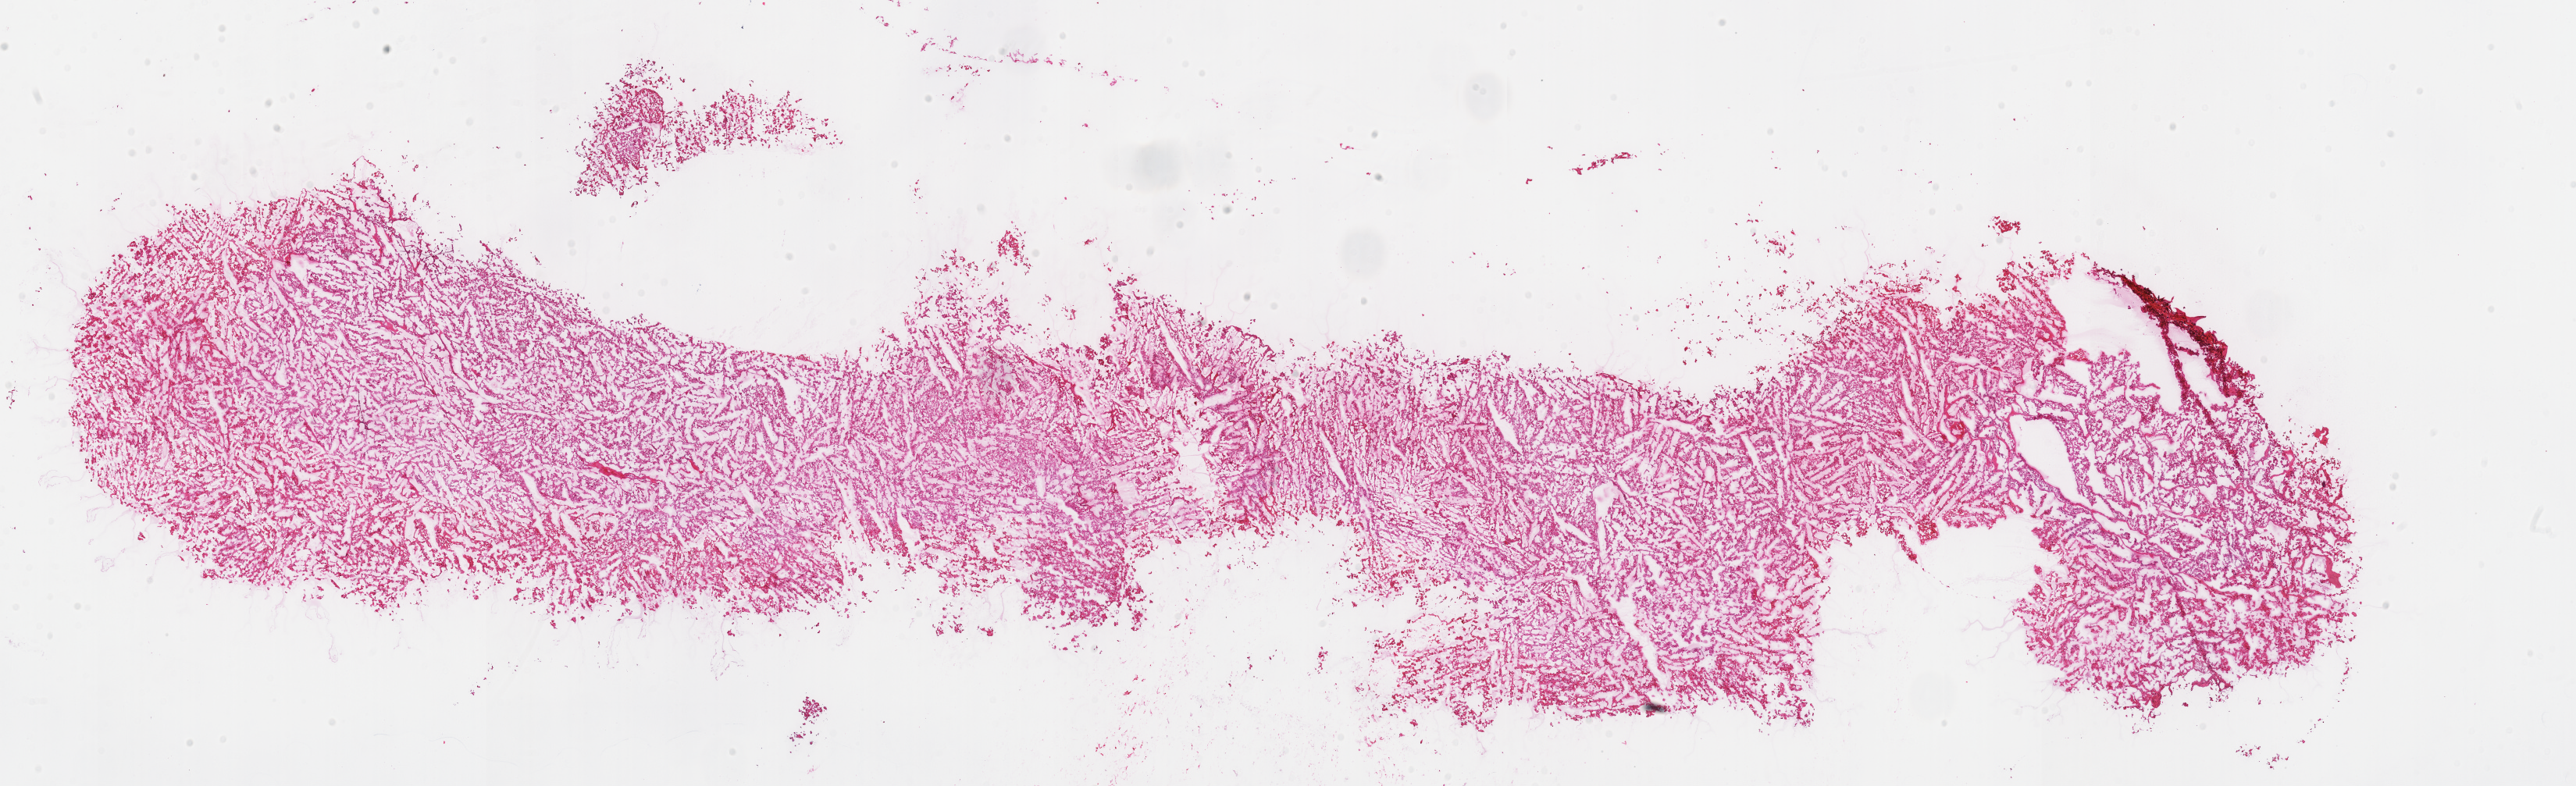
Digitized Hematoxylin and eosin (H&E) stained tissue section (whole slide) — shown as a low-resolution overview of the whole scanned area (about 25.9 x 7.9 mm), frozen section, sample: primary tumour, kidney. Female, age 44 years at initial diagnosis. Pathologist review of this section (percent, as recorded): tumour cells 90%, tumour nuclei 90%, normal cells 0%, stromal cells 10%, necrosis 0%.
* pathologic diagnosis: Renal cell carcinoma, chromophobe type
* TNM: T1 N0 M0
* AJCC pathologic stage: I (7th edition)